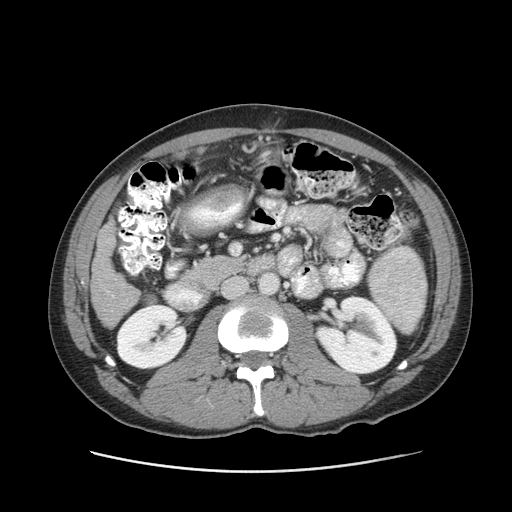
Contrast-enhanced abdominal CT (liver protocol), one axial slice; slice 31 of 93 in the series (ordered by position); soft-tissue window (W 400 / L 40 HU); 2.5 mm slice thickness; 512 × 512 image matrix, field of view 380 × 380 mm. Case-level facts recorded for this patient, not image findings: diagnosis: hepatocellular carcinoma (patient treated with transarterial chemoembolisation; whether this scan precedes or follows treatment is not stated here); TNM stage (as recorded): Stage-II; Child-Pugh class: A; tumour differentiation: moderately differentiated; tumour nodularity: multinodular.
Annotated regions visible in this slice (semi-automatic segmentation, software-assisted and operator-edited):
- liver parenchyma outside the tumour (the mass and vessels are separate outlines, so this box may not span the whole liver): bounding box (x1, y1, x2, y2) in pixels: (92, 219, 138, 326)